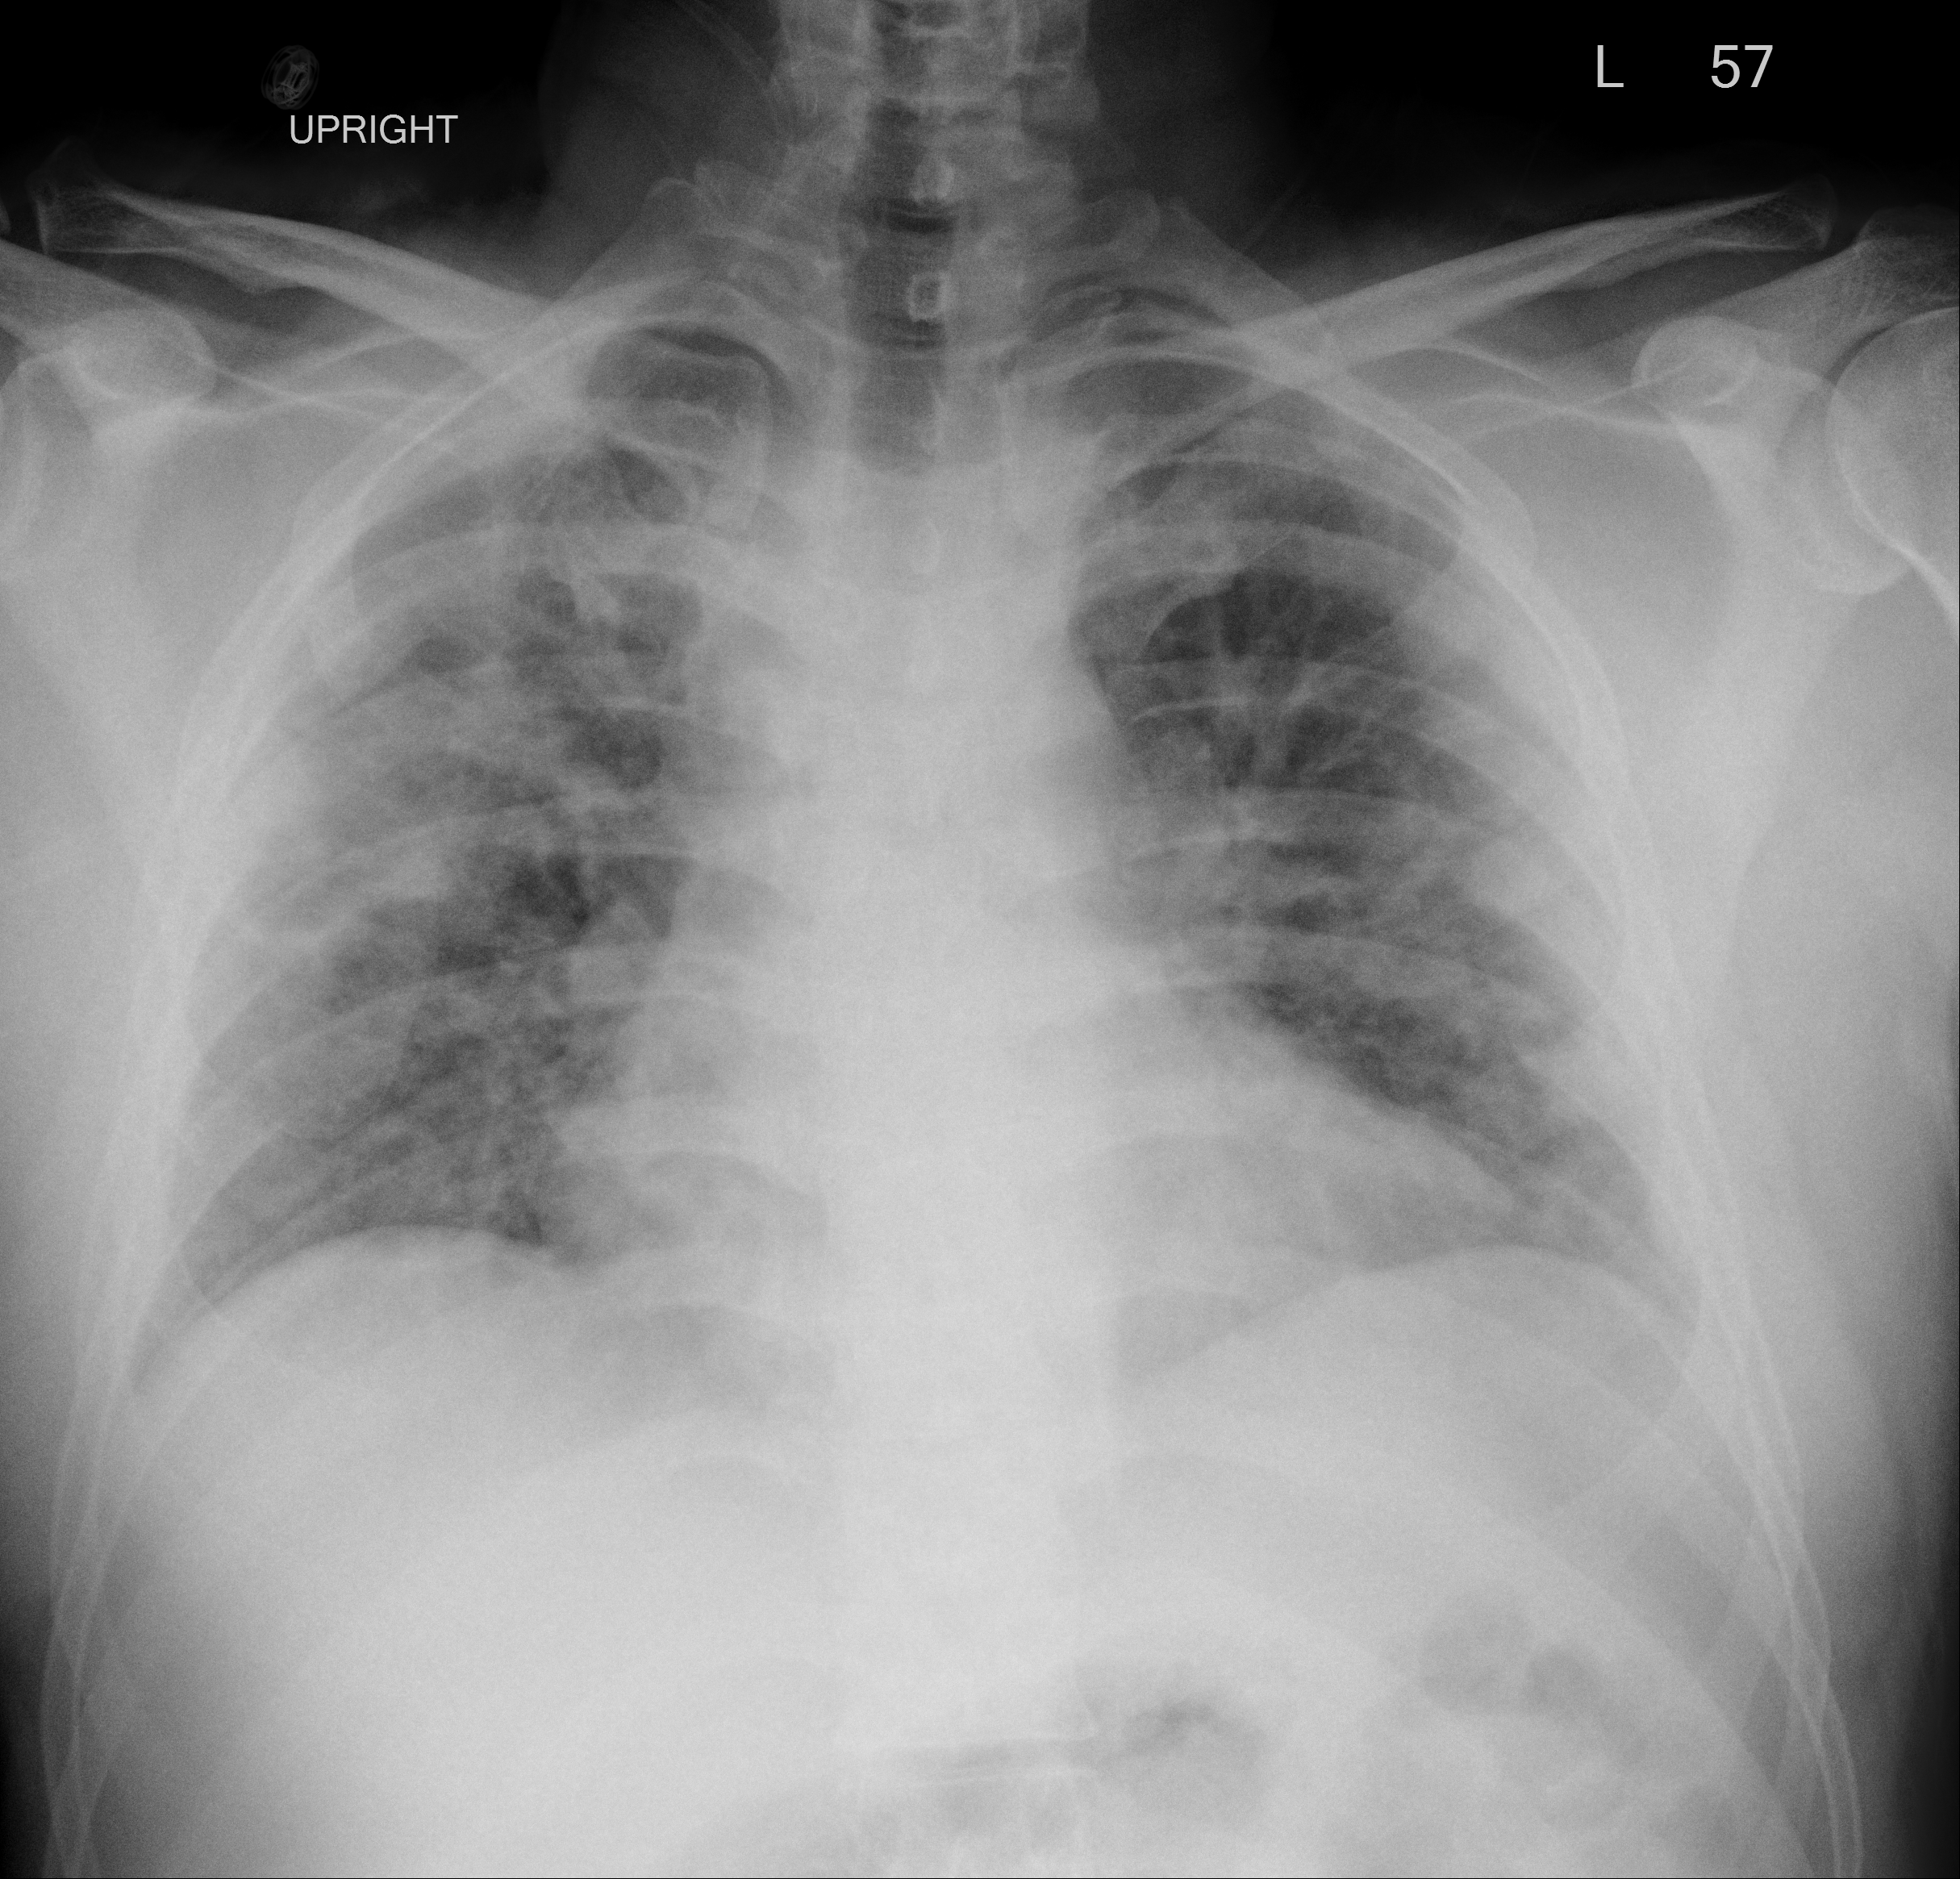
Chest X-ray (portable), AP projection. Male patient, age 41 years; COVID-19 (test-positive).
Key findings recorded by the radiologist: Lungs are moderately inflated but there are worsening ill-defined infiltrates predominately in the periphery of both lungs.